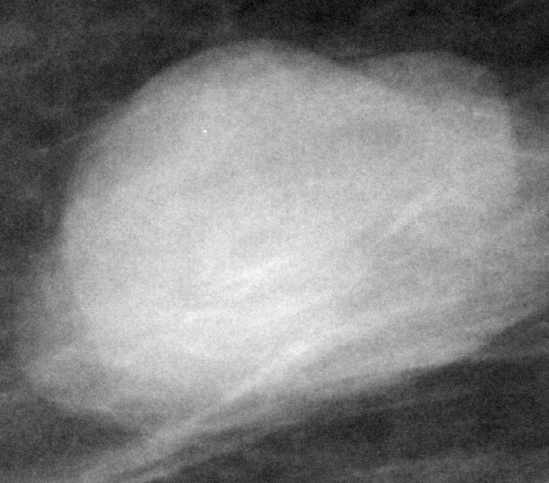
Cropped region of a digitized screen-film mammogram centred on a radiologist-marked abnormality, right breast, MLO view, BI-RADS breast density category 1 (scale 1–4).
Mass, shape lobulated, margins circumscribed; BI-RADS assessment category 4; subtlety rating 5 on a 1 (subtle) to 5 (obvious) scale; pathology result (as recorded, not read from the image): benign.